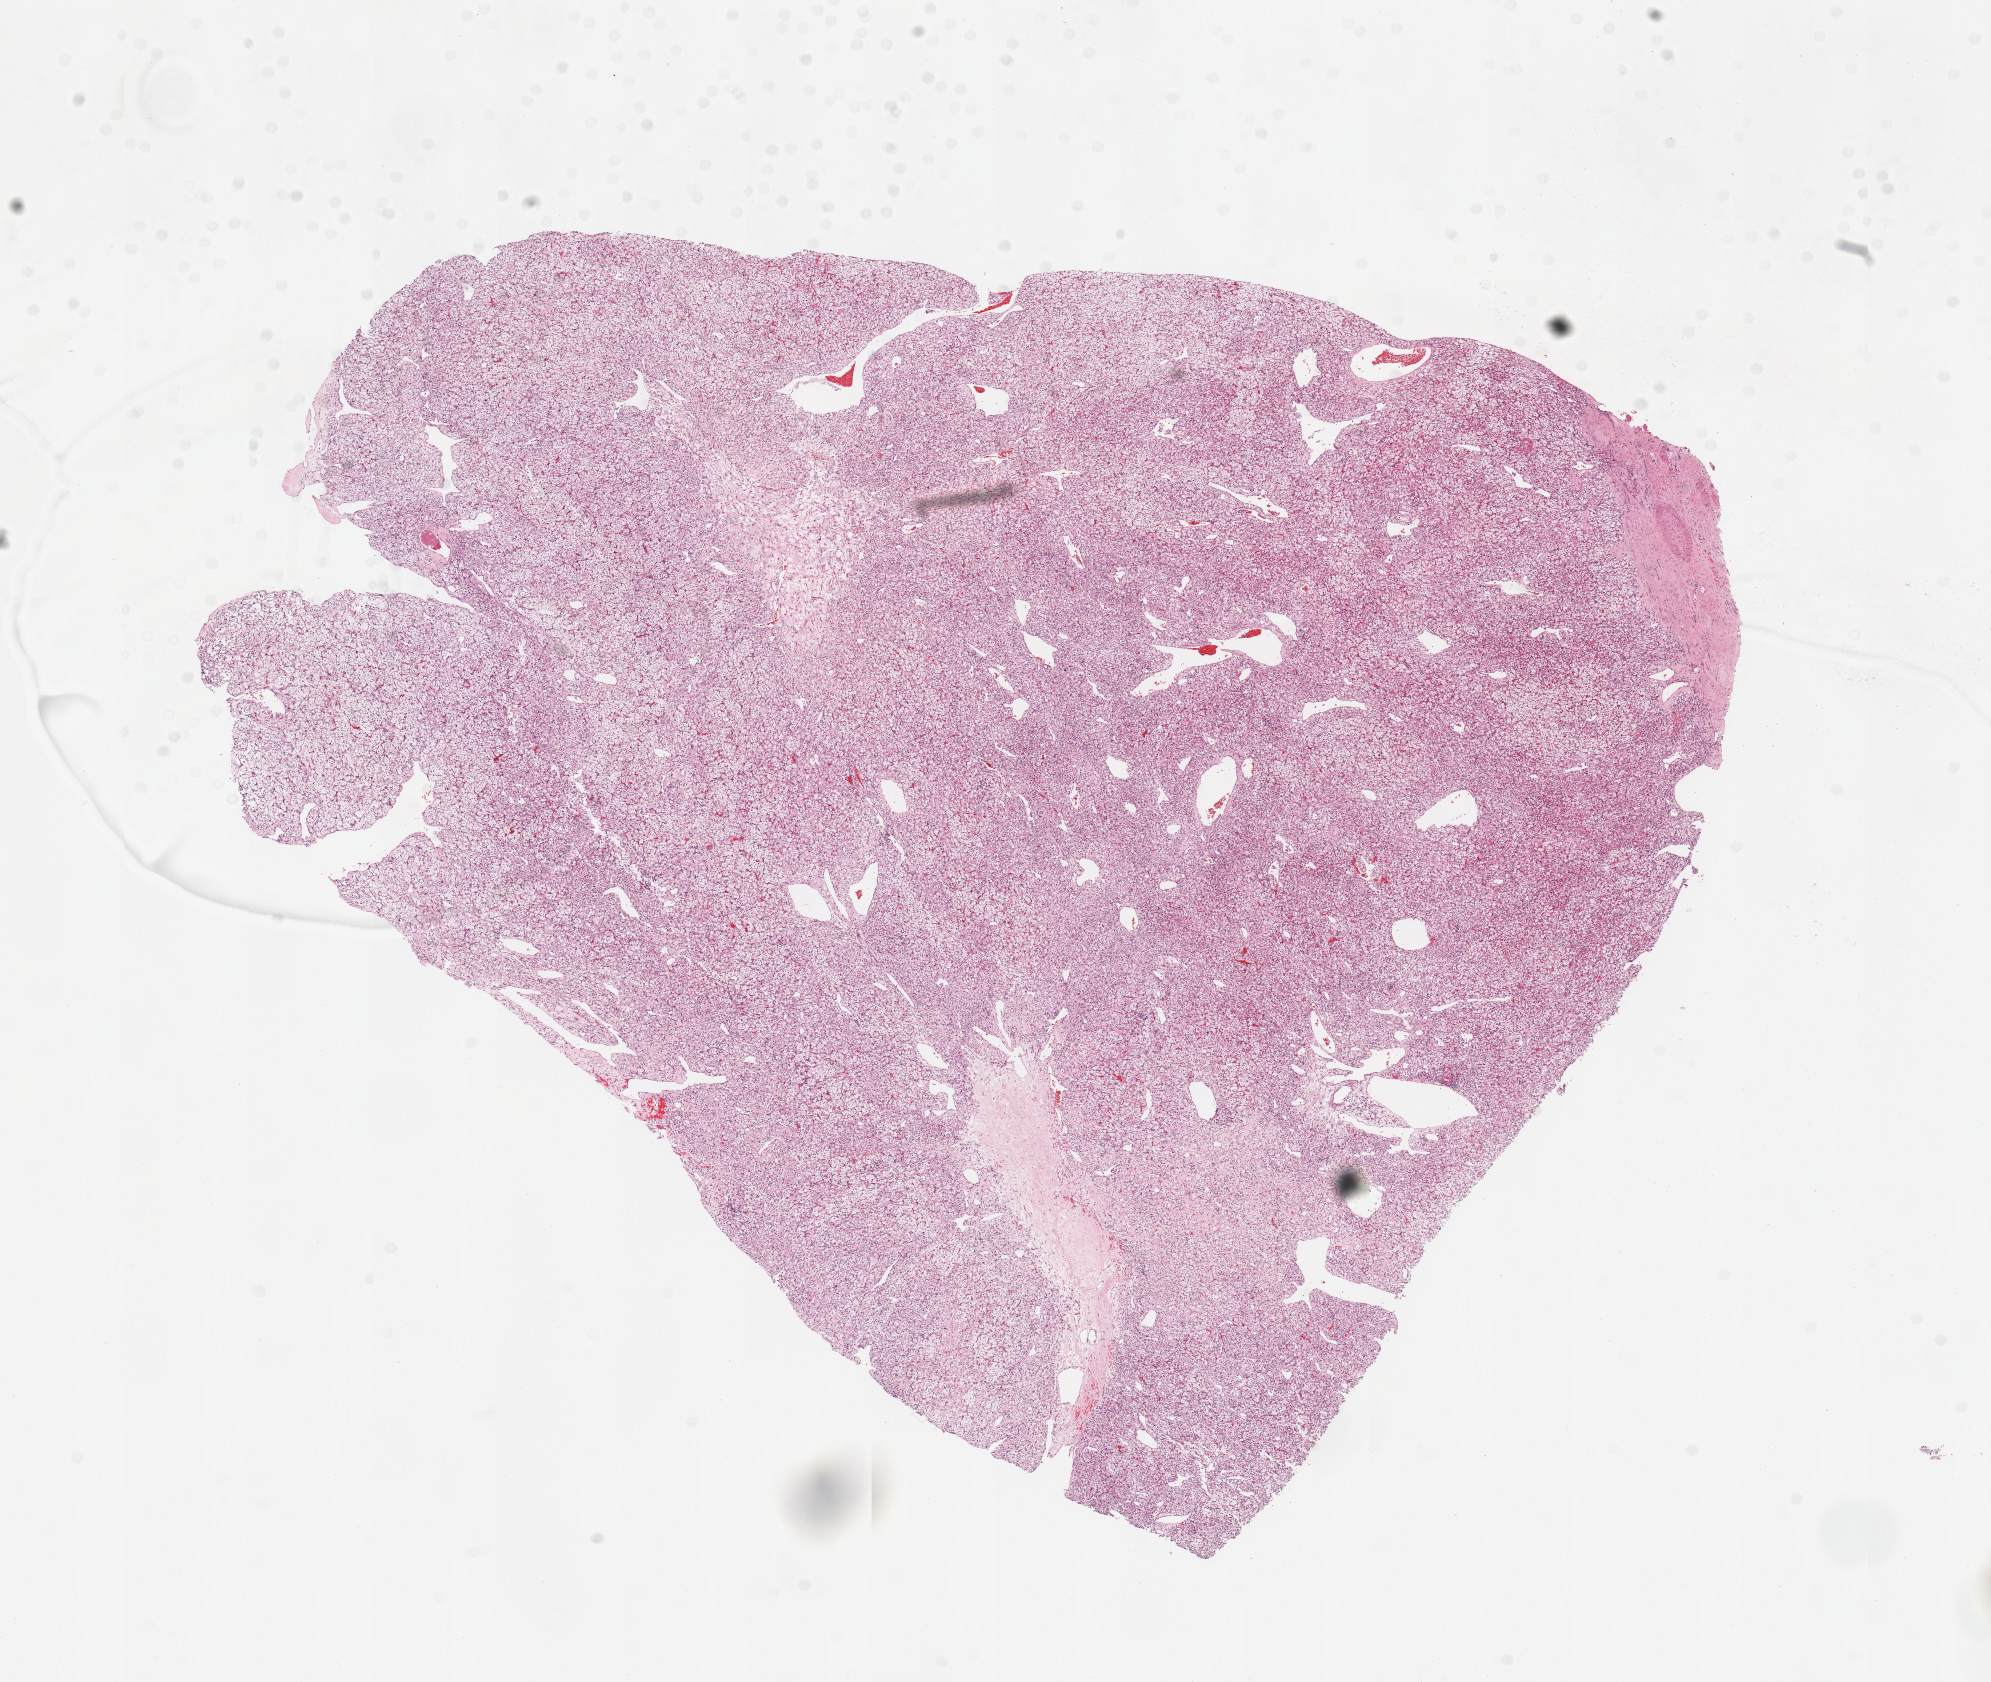
Digitized H&E tissue section (whole slide), low-resolution overview of the scanned area, about 15.8 x 13.3 mm (acquisition: 20x scan). Tumour tissue sample, sampled site: kidney. 72-year-old male patient. Histologic grade: G2 (moderately differentiated). Composition of this section per pathologist review: tumour nuclei 95%, necrosis 0%.
• diagnosis: Renal cell carcinoma, NOS
• primary tumour site (as recorded): middle
• AJCC pathologic stage: III